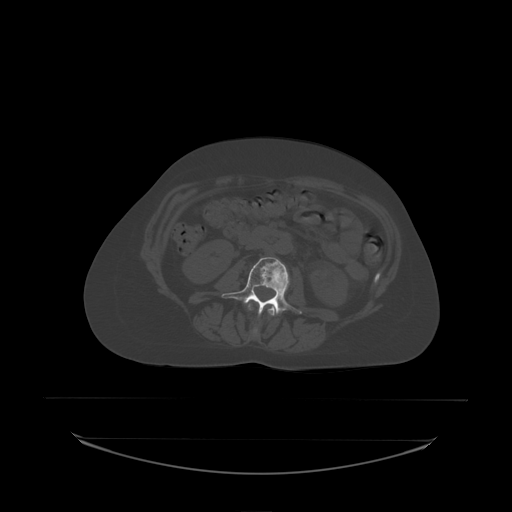
CT including the spine, one axial slice; slice 63 of 242 in the series (ordered by position); bone window (W 1800 / L 400 HU); 2.5 mm slice thickness; 512 × 512 image matrix, field of view 500 × 500 mm. Patient: female, 53 years. From the clinical record (not read from this slice): primary cancer: lung; vertebrae with lytic lesions (as recorded): T7, L1.
Annotated regions visible in this slice (semi-automatic segmentation, software-assisted and operator-edited):
- L2 vertebra: bounding box <248,304,277,316> (left, top, right, bottom; pixels)
- L3 vertebra: <222,257,302,316>